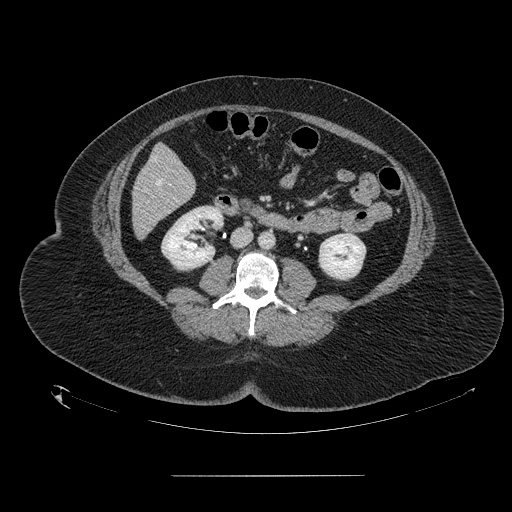
Contrast-enhanced abdominal CT, one axial slice. Position 41 of 164 along the scan axis. Intravenous contrast given. Soft-tissue window (W 400 / L 40 HU). 2.5 mm slice thickness. 512 × 512 image matrix, field of view 495 × 495 mm. Female patient, age 52 years. Case-level facts recorded for this patient, not image findings: diagnosis: colorectal cancer liver metastases, imaged before liver resection; multiple liver metastases: yes; largest metastasis: 3.5 cm; chemotherapy before resection: no.
Outlined on this slice (outlined manually by an expert reader):
- hepatic veins: bounding box <156,179,162,185> (left, top, right, bottom; pixels)
- liver: <133,146,195,237>